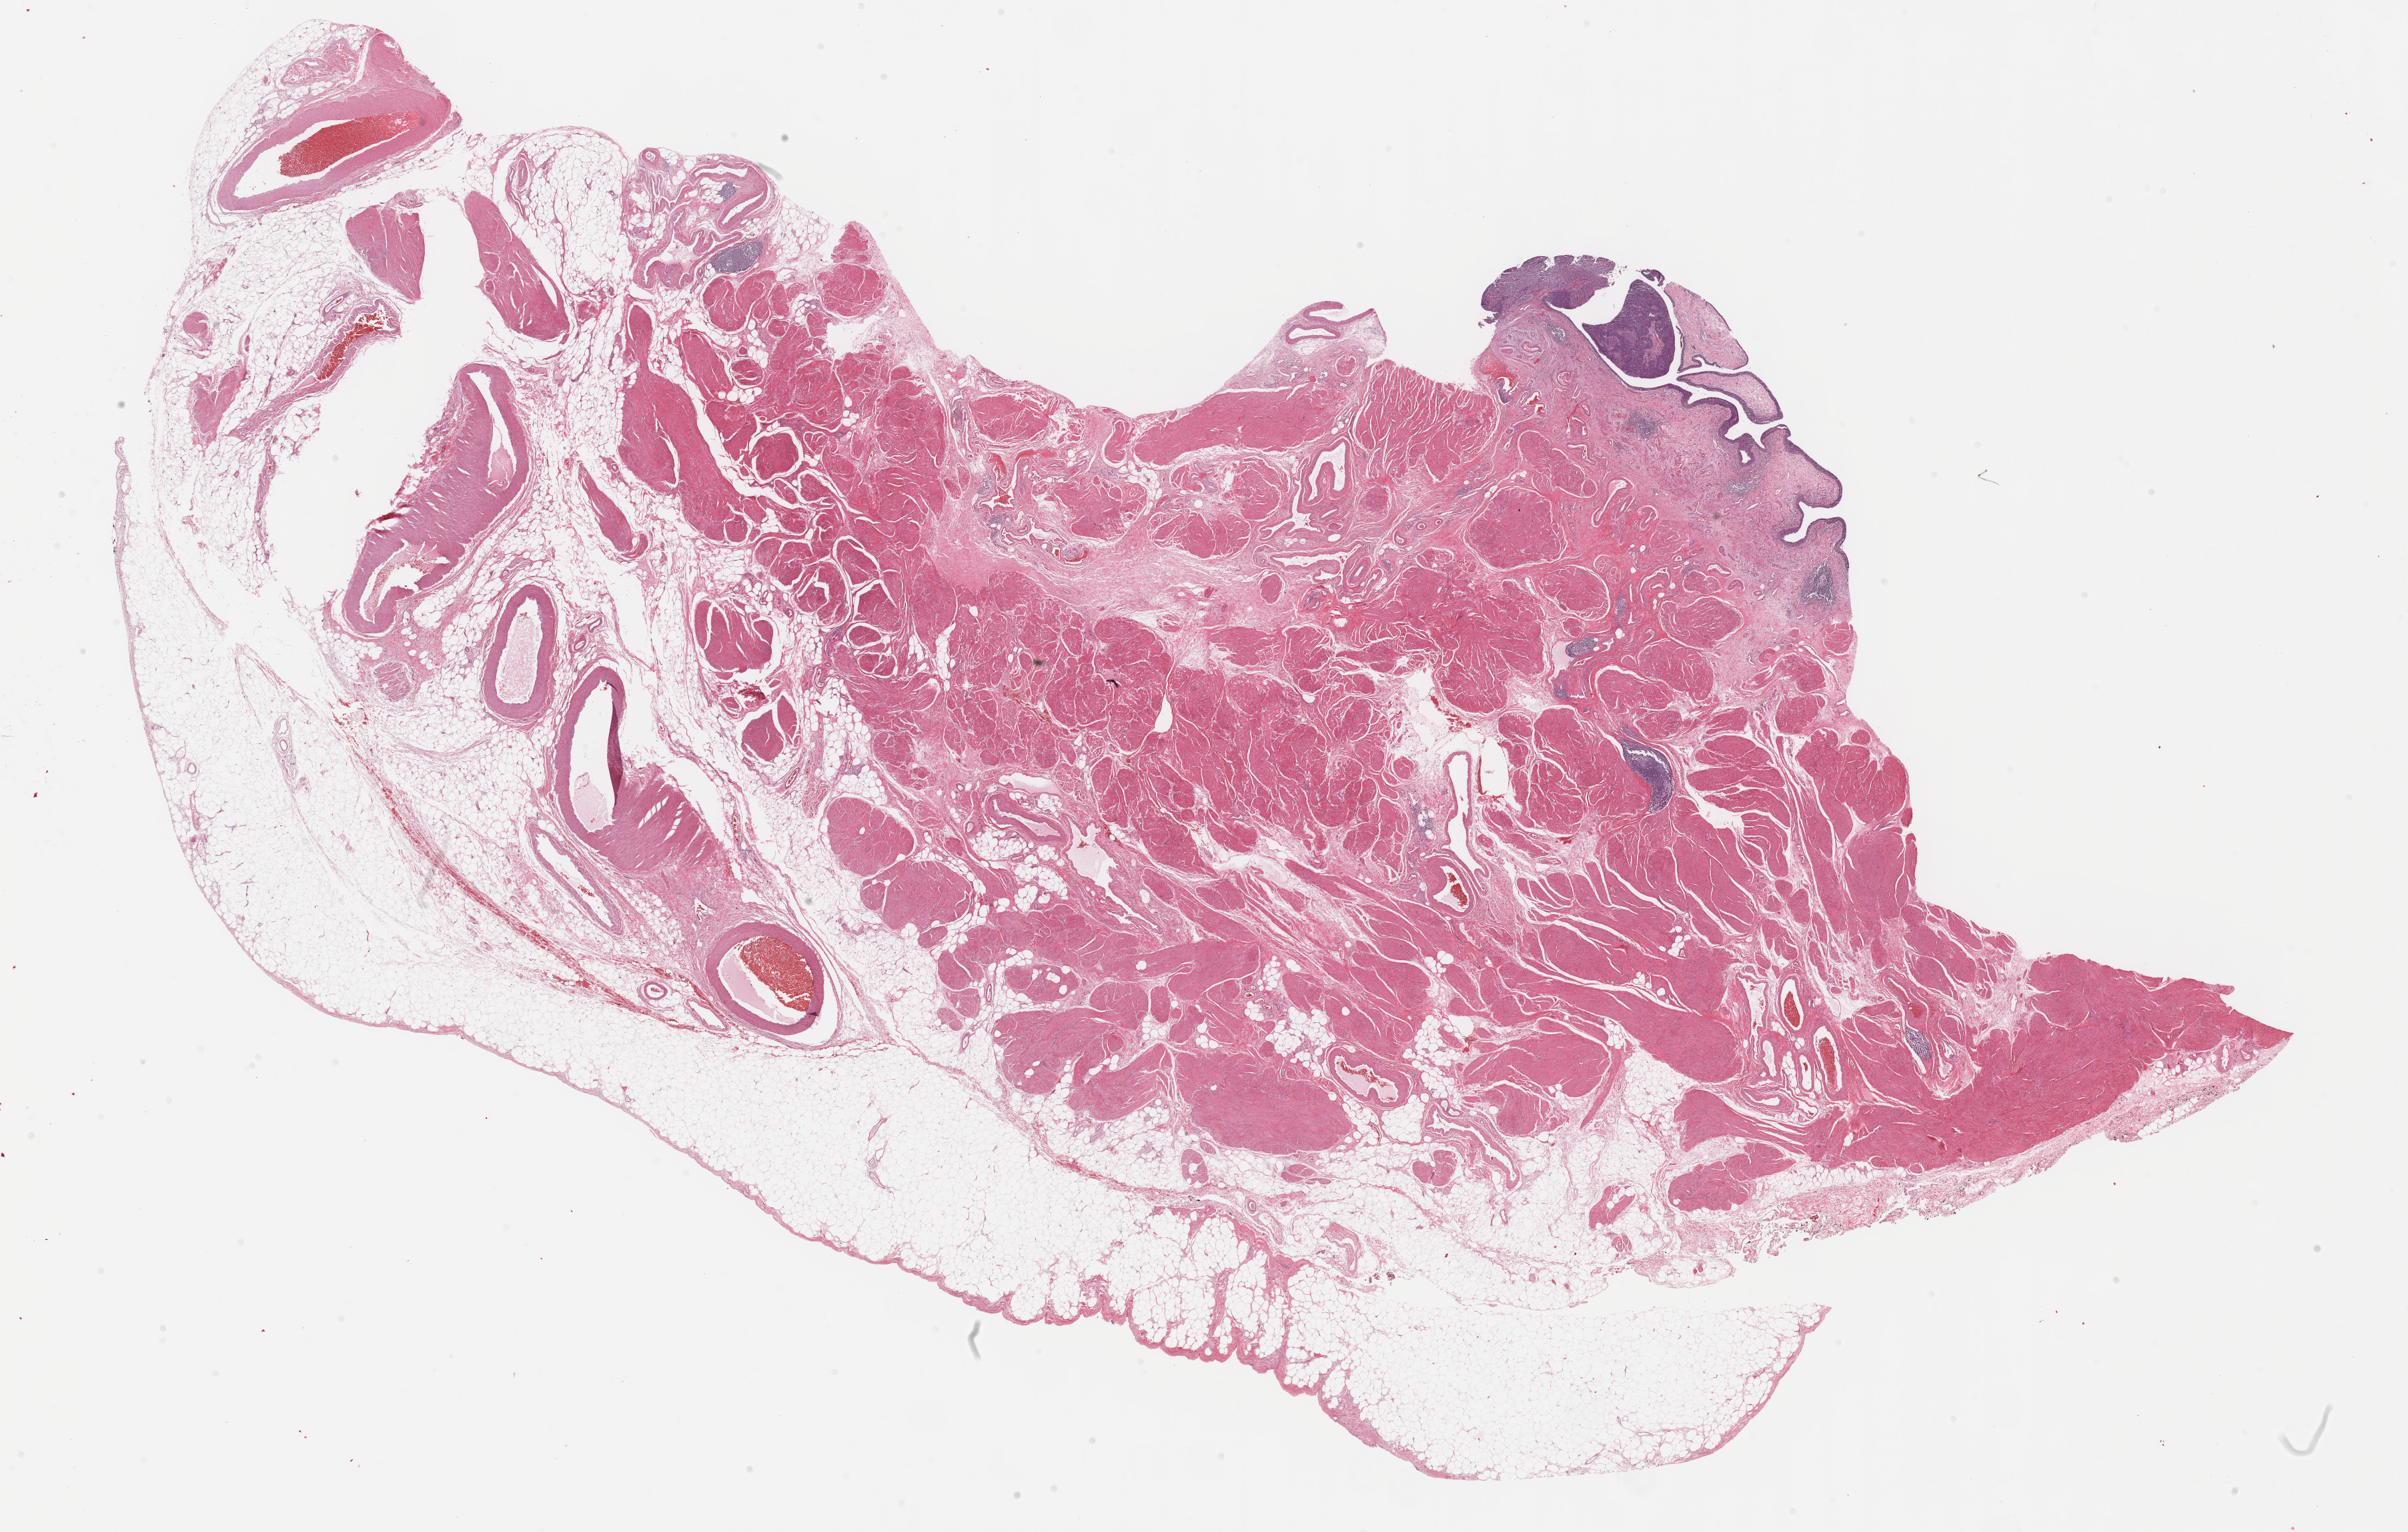
Digitized H&E tissue section (whole slide) — shown as a low-resolution overview of the whole scanned area (about 29.2 x 18.6 mm), FFPE section, primary tumour sample from the bladder. Patient: female, age at initial diagnosis 50 years. Histologic grade: high grade.
TNM: T2b N0 MX. Pathologic diagnosis: Papillary transitional cell carcinoma. AJCC pathologic stage: II.